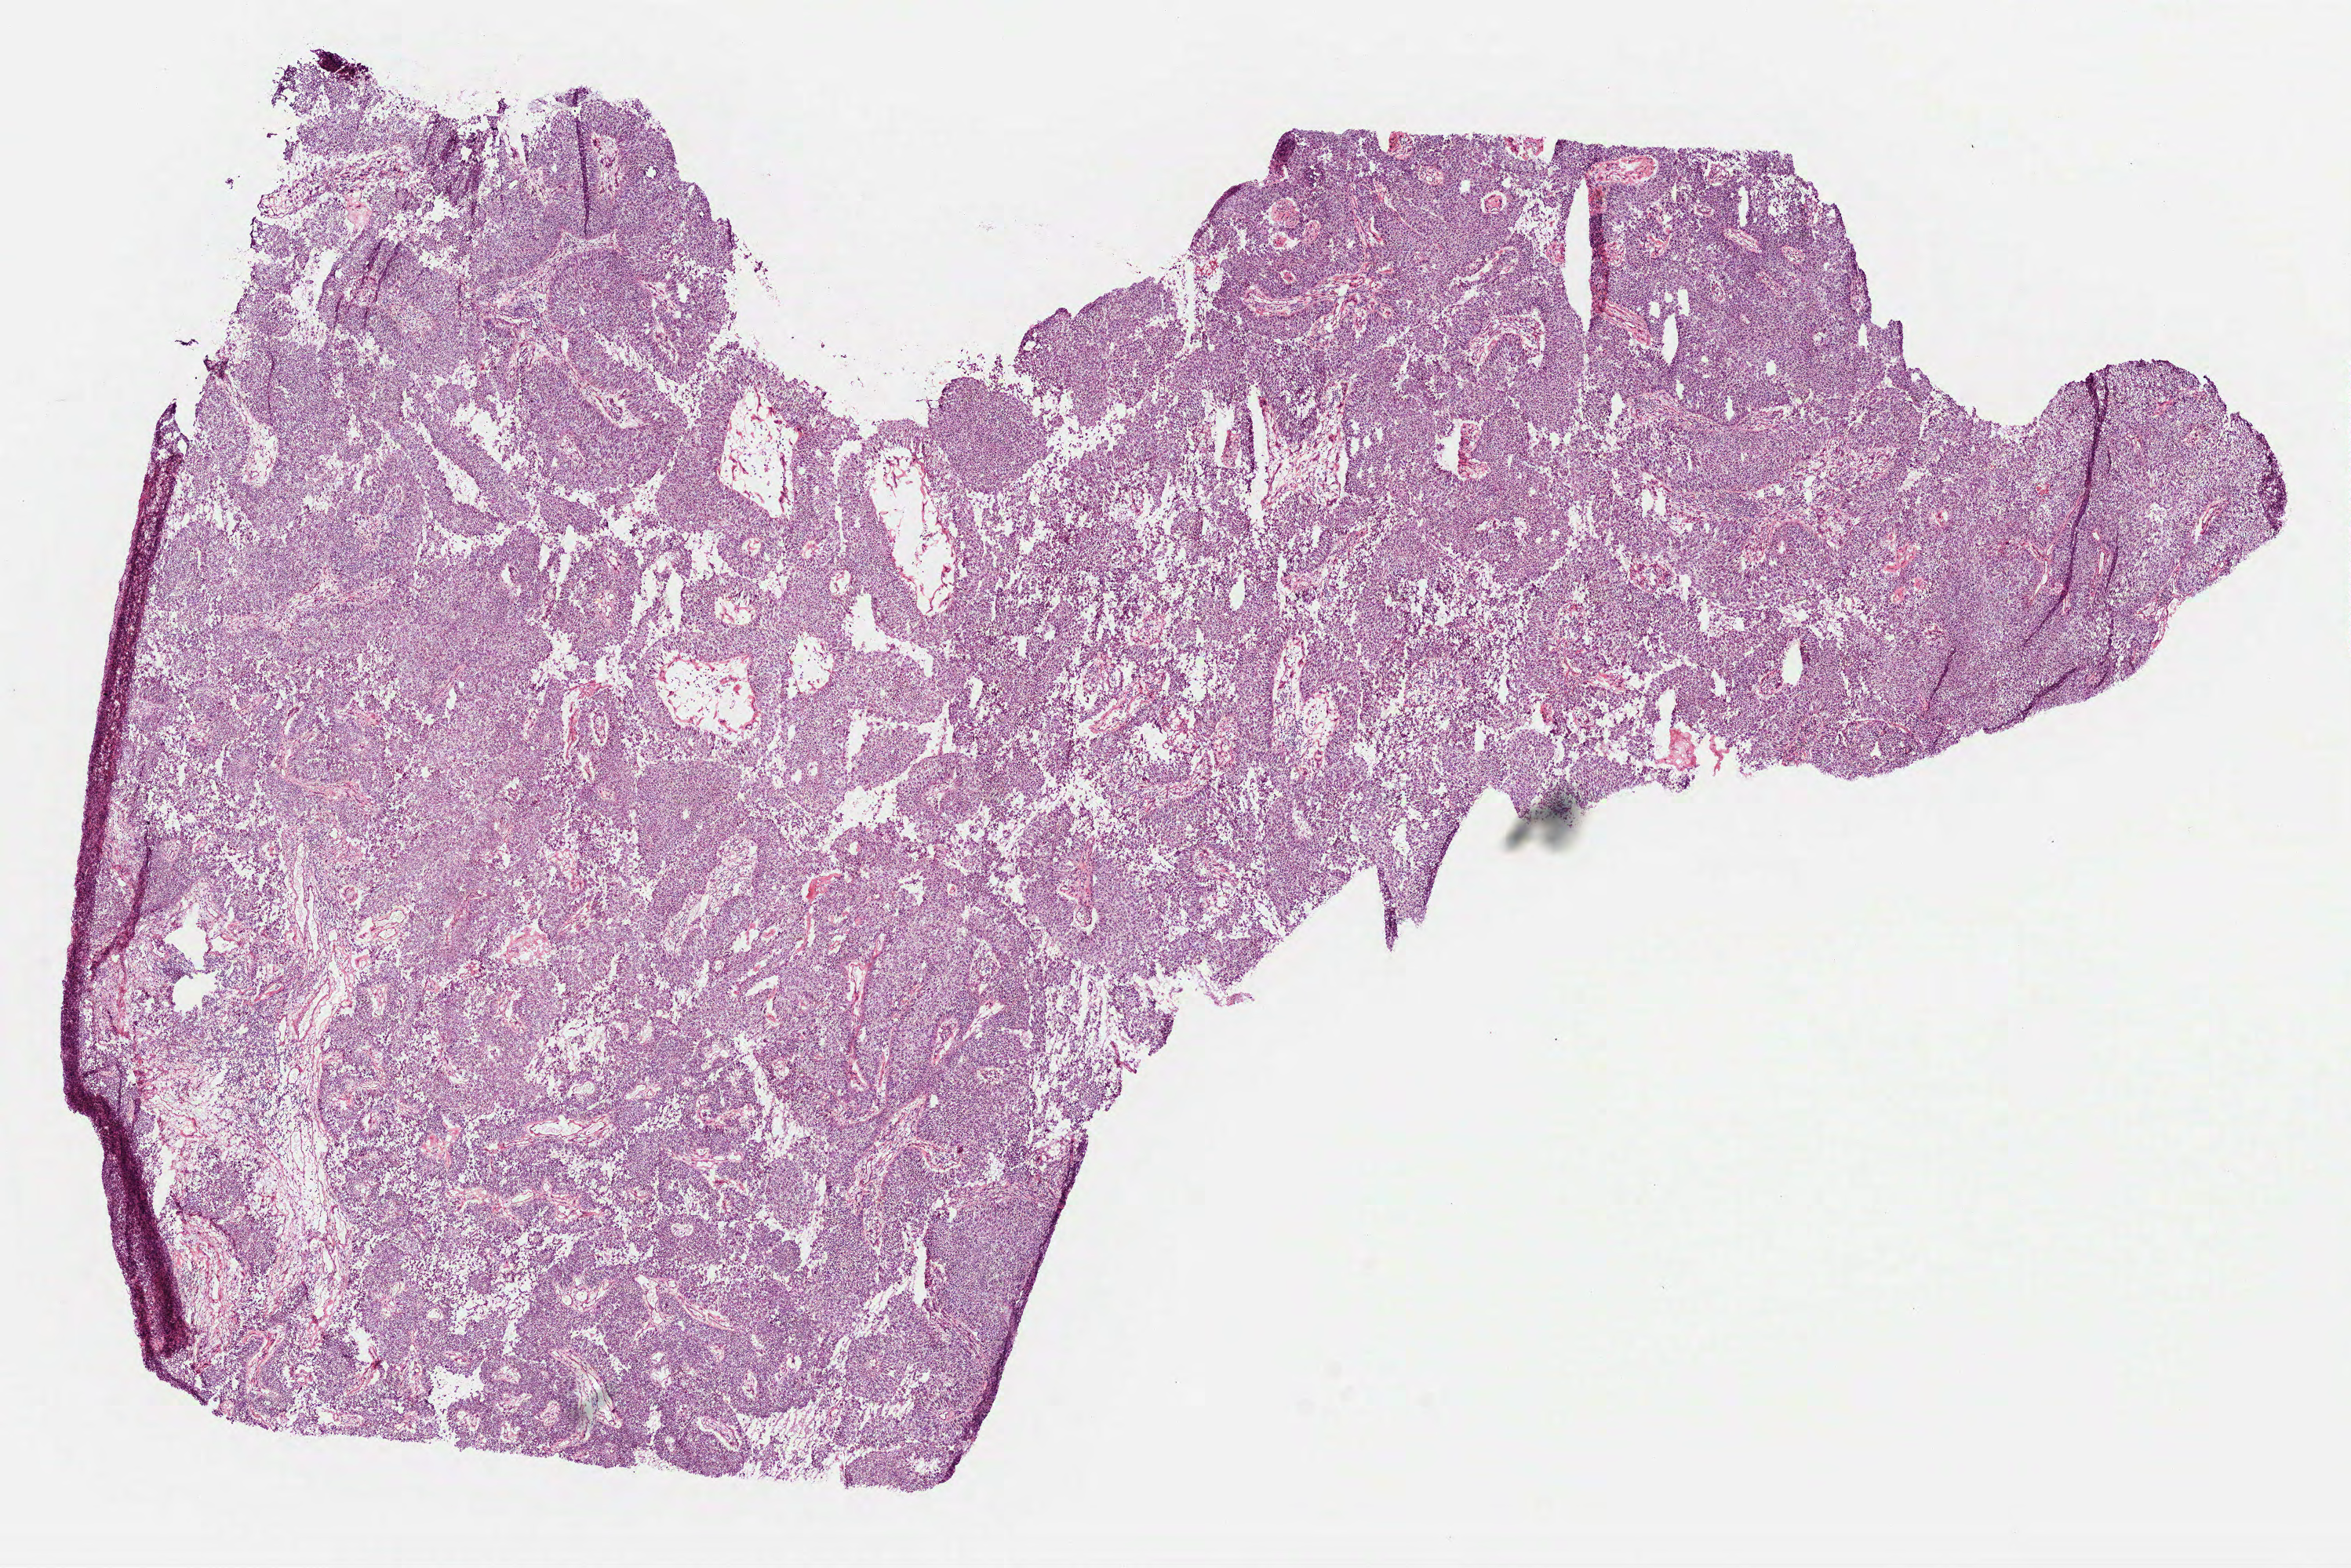
H&E-stained whole-slide image — low-resolution overview of the scanned area, about 12.1 x 8.1 mm (slide scanned at 40x). Frozen section from the bottom of the tissue portion. Sample: primary tumour, kidney. Female patient. Slide review estimates, as recorded: tumour cells 100%, tumour nuclei 85%.
Histologic diagnosis: Papillary adenocarcinoma, NOS.